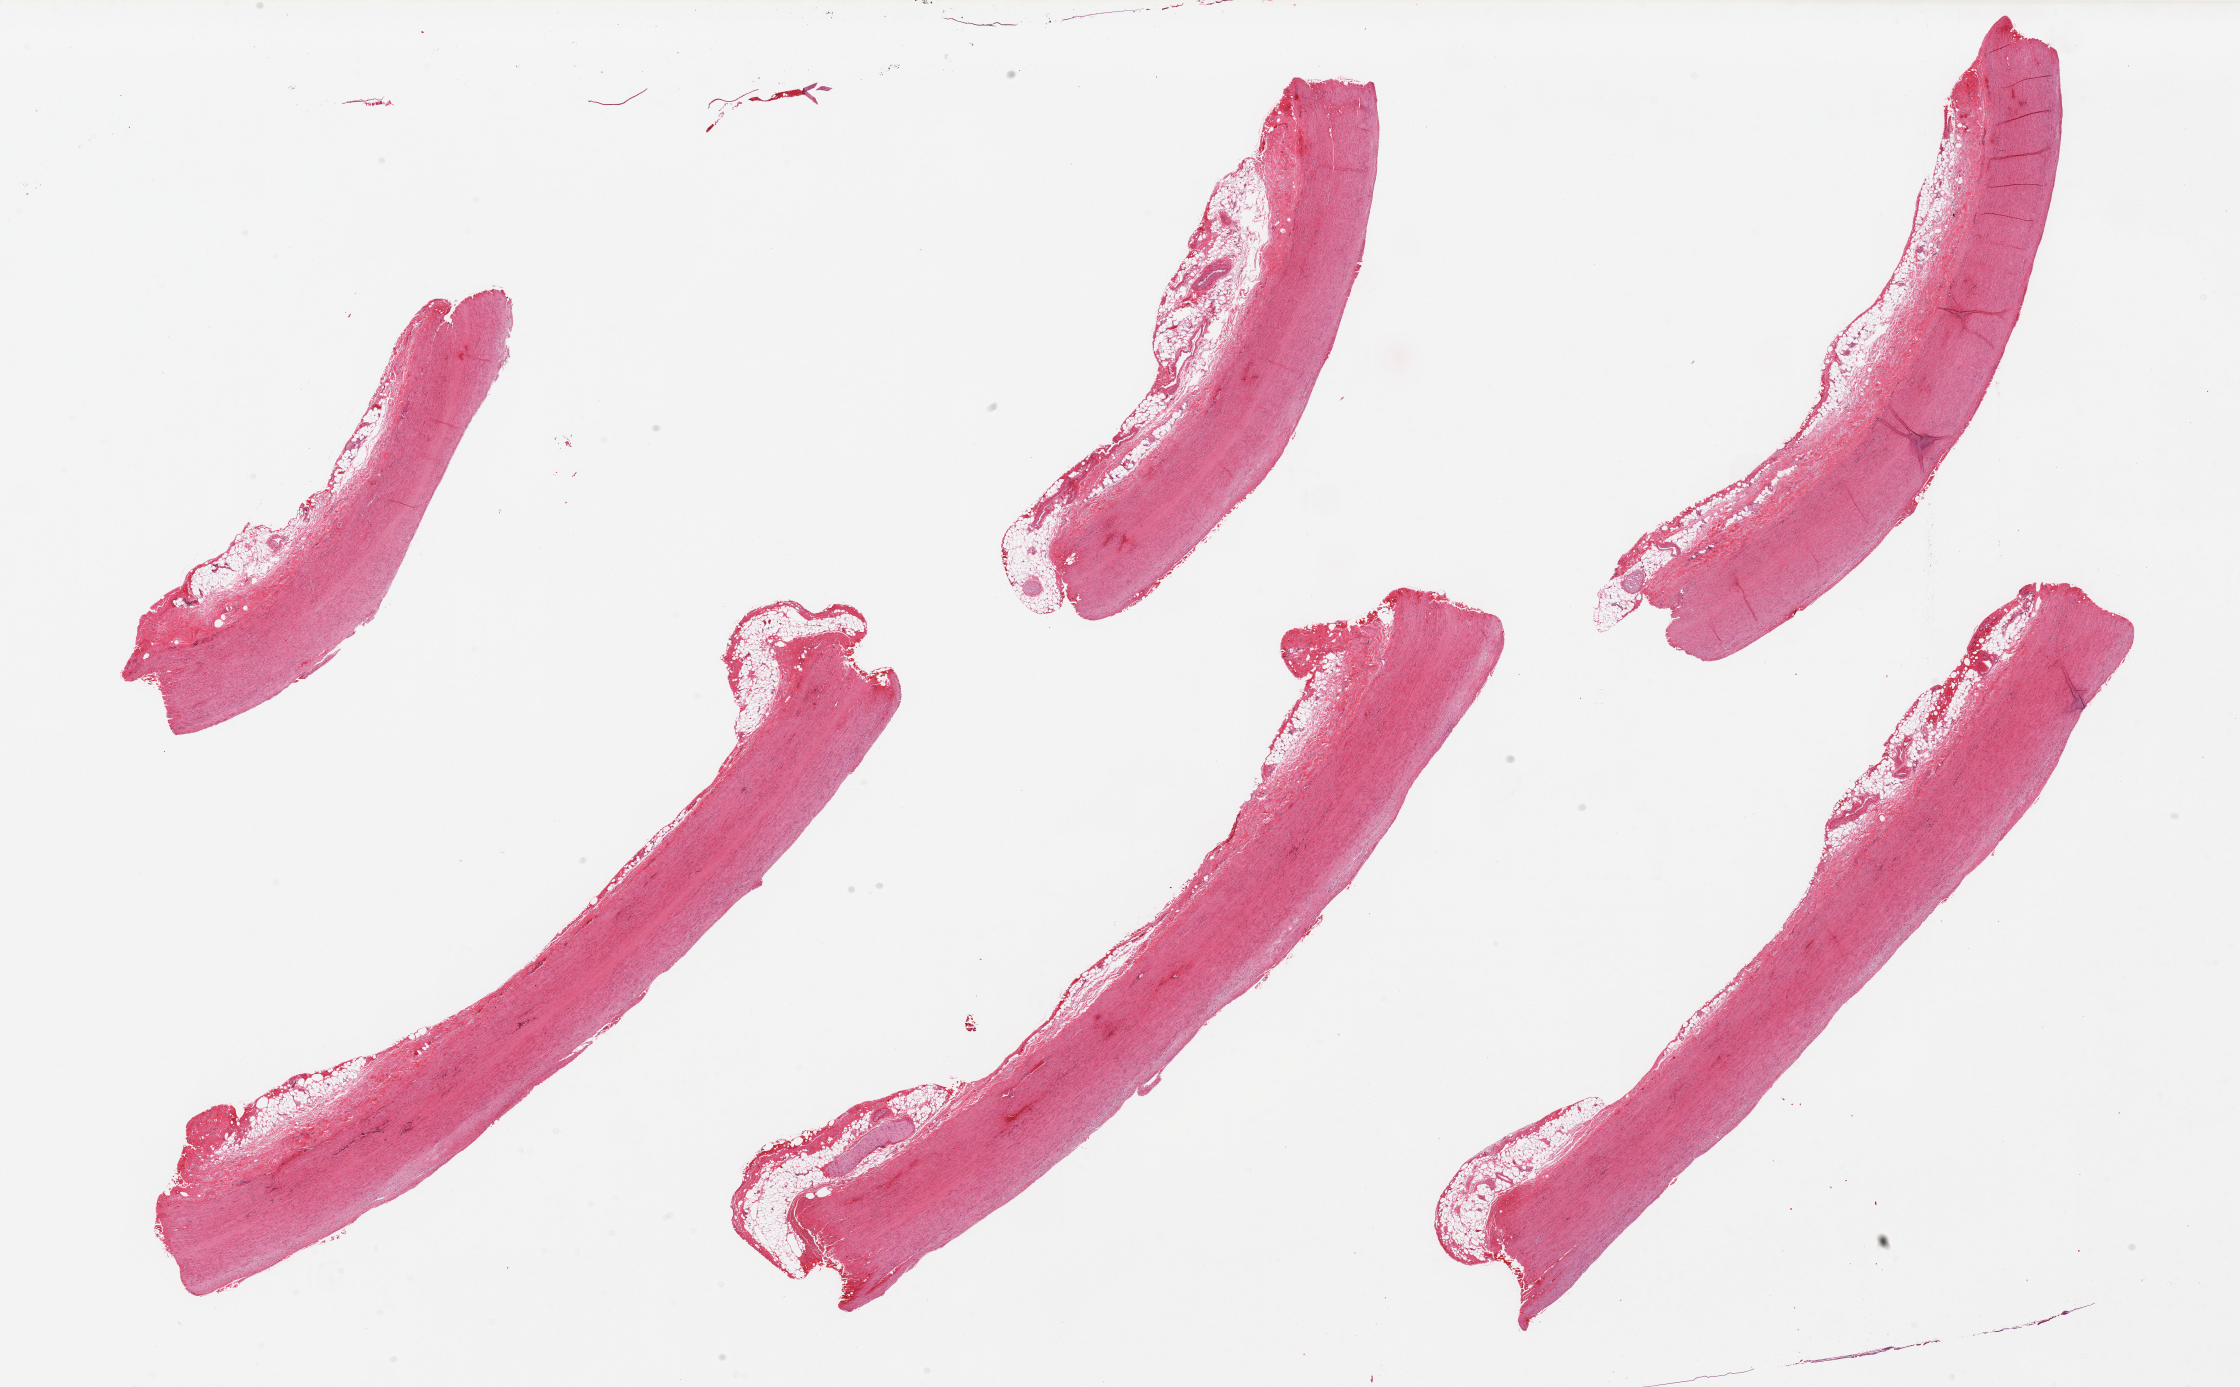
Digitized haematoxylin and eosin-stained section, brightfield, shown as a low-resolution overview of the whole scanned area (about 35.4 x 21.9 mm, acquisition: 20x scan), PAXgene-fixed paraffin-embedded (PFPE) section, sampled site (target tissue): aorta, tissue donor sample. Donor sex: male.
Pathologist's review note for this sample: 6 pieces, attached adventitia/fat, atherosclerosis.